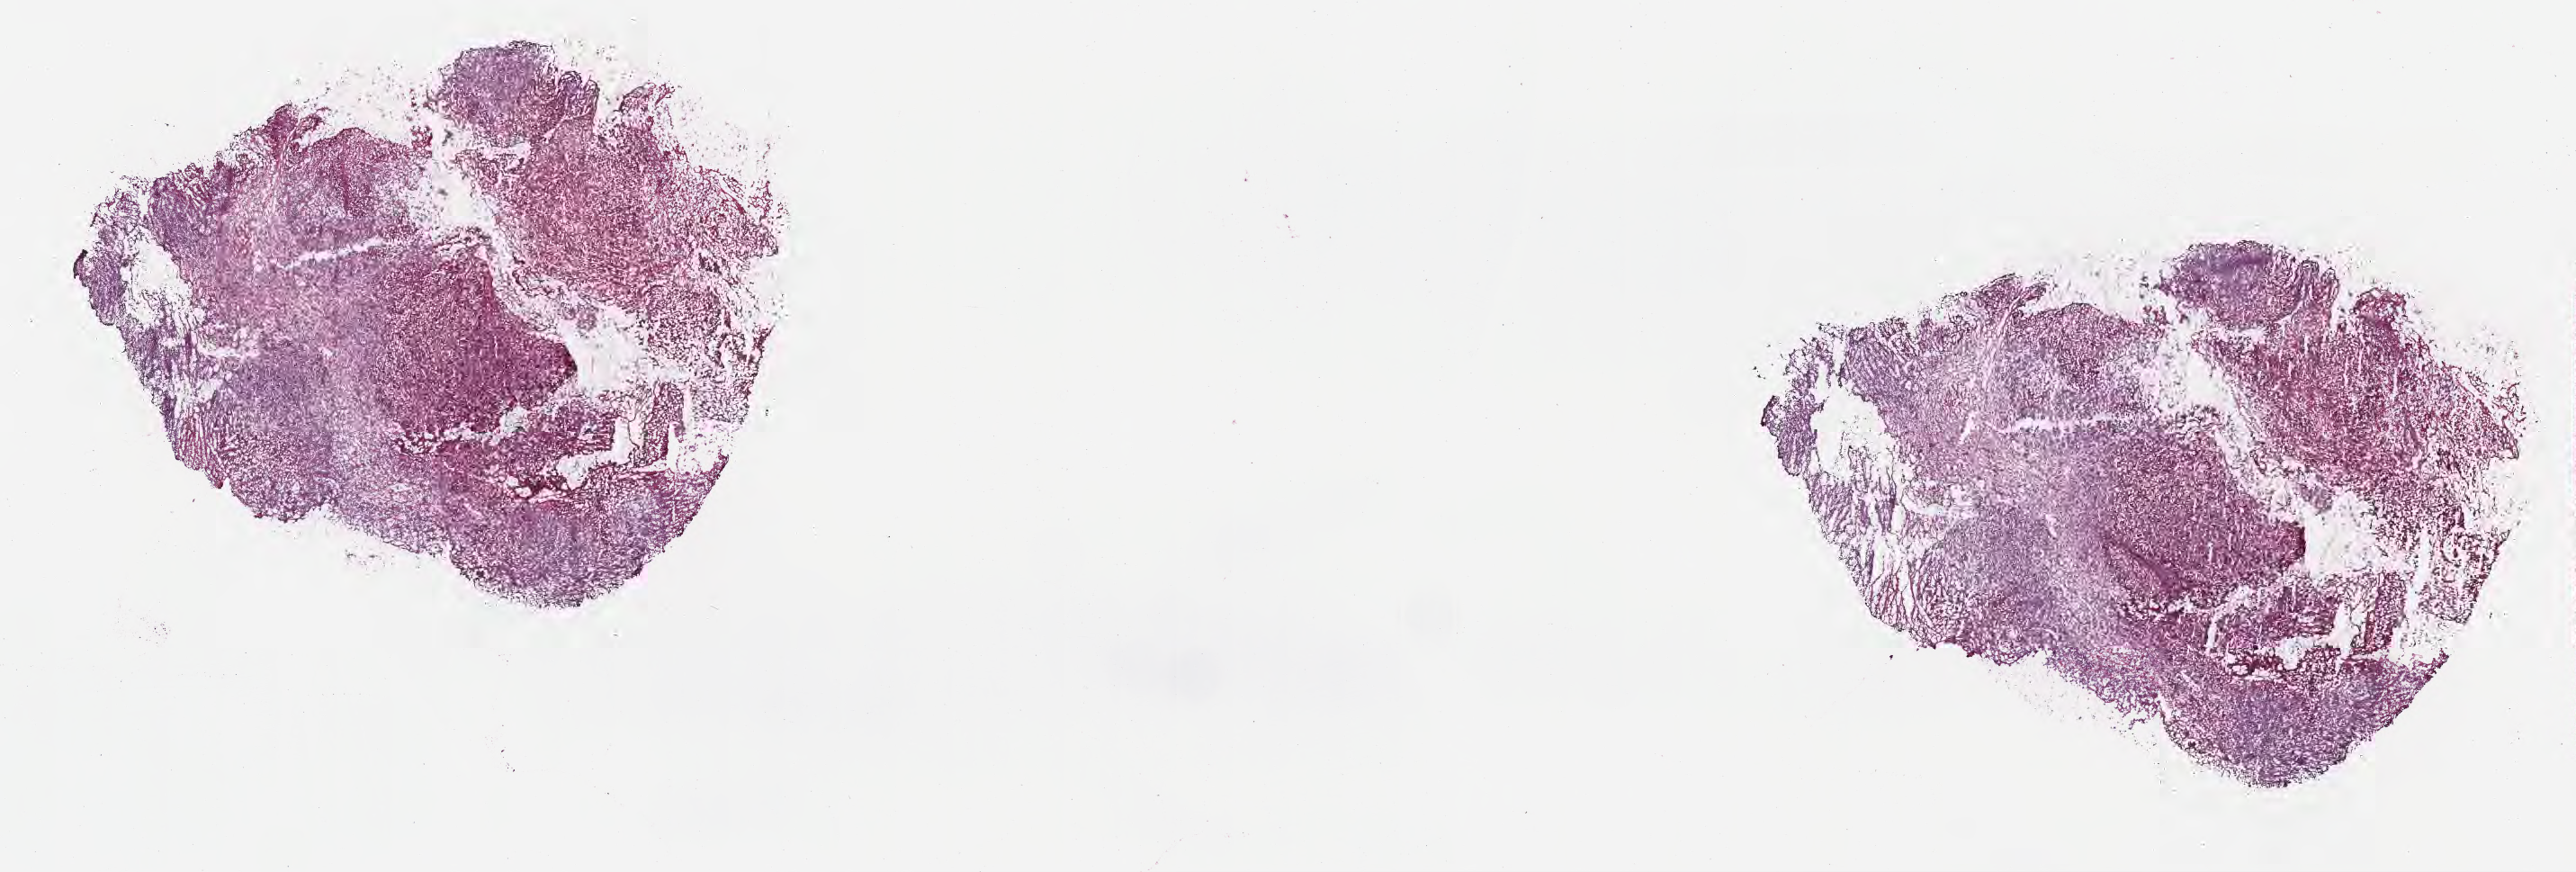
Whole-slide image, H&E stain — a low-resolution overview of the entire scanned area, about 23.2 x 7.8 mm, frozen section (tissue freezing medium), metastatic tumor tissue, resected from small intestine. Male patient; age at initial diagnosis 58 years. Slide review estimates, as recorded: tumor cells 40%, tumor nuclei 80%, stromal cells 5%, necrosis 40%, normal cells 15%. Inflammatory infiltration, as recorded: lymphocyte infiltration 5%, monocyte infiltration 2%, neutrophil infiltration 8%.
- patient diagnosis (primary): Malignant melanoma, NOS